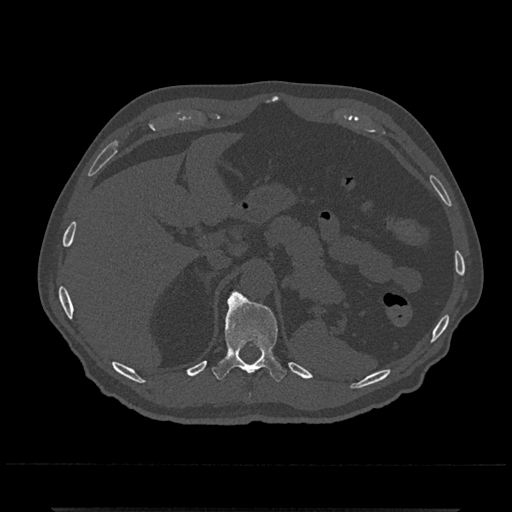
CT including the spine, one axial slice. Slice 496 of 797 in the series (ordered by position). Reconstruction kernel Br40s/3. Bone window (W 1800 / L 400 HU). 512 × 512 image matrix, field of view 393 × 393 mm. Male patient, age 67 years. From the clinical record (not read from this slice): primary cancer: prostate.
Annotated regions visible in this slice (semi-automatic segmentation, software-assisted and operator-edited):
- T11 vertebra: bounding box <212,289,287,383> (left, top, right, bottom; pixels)